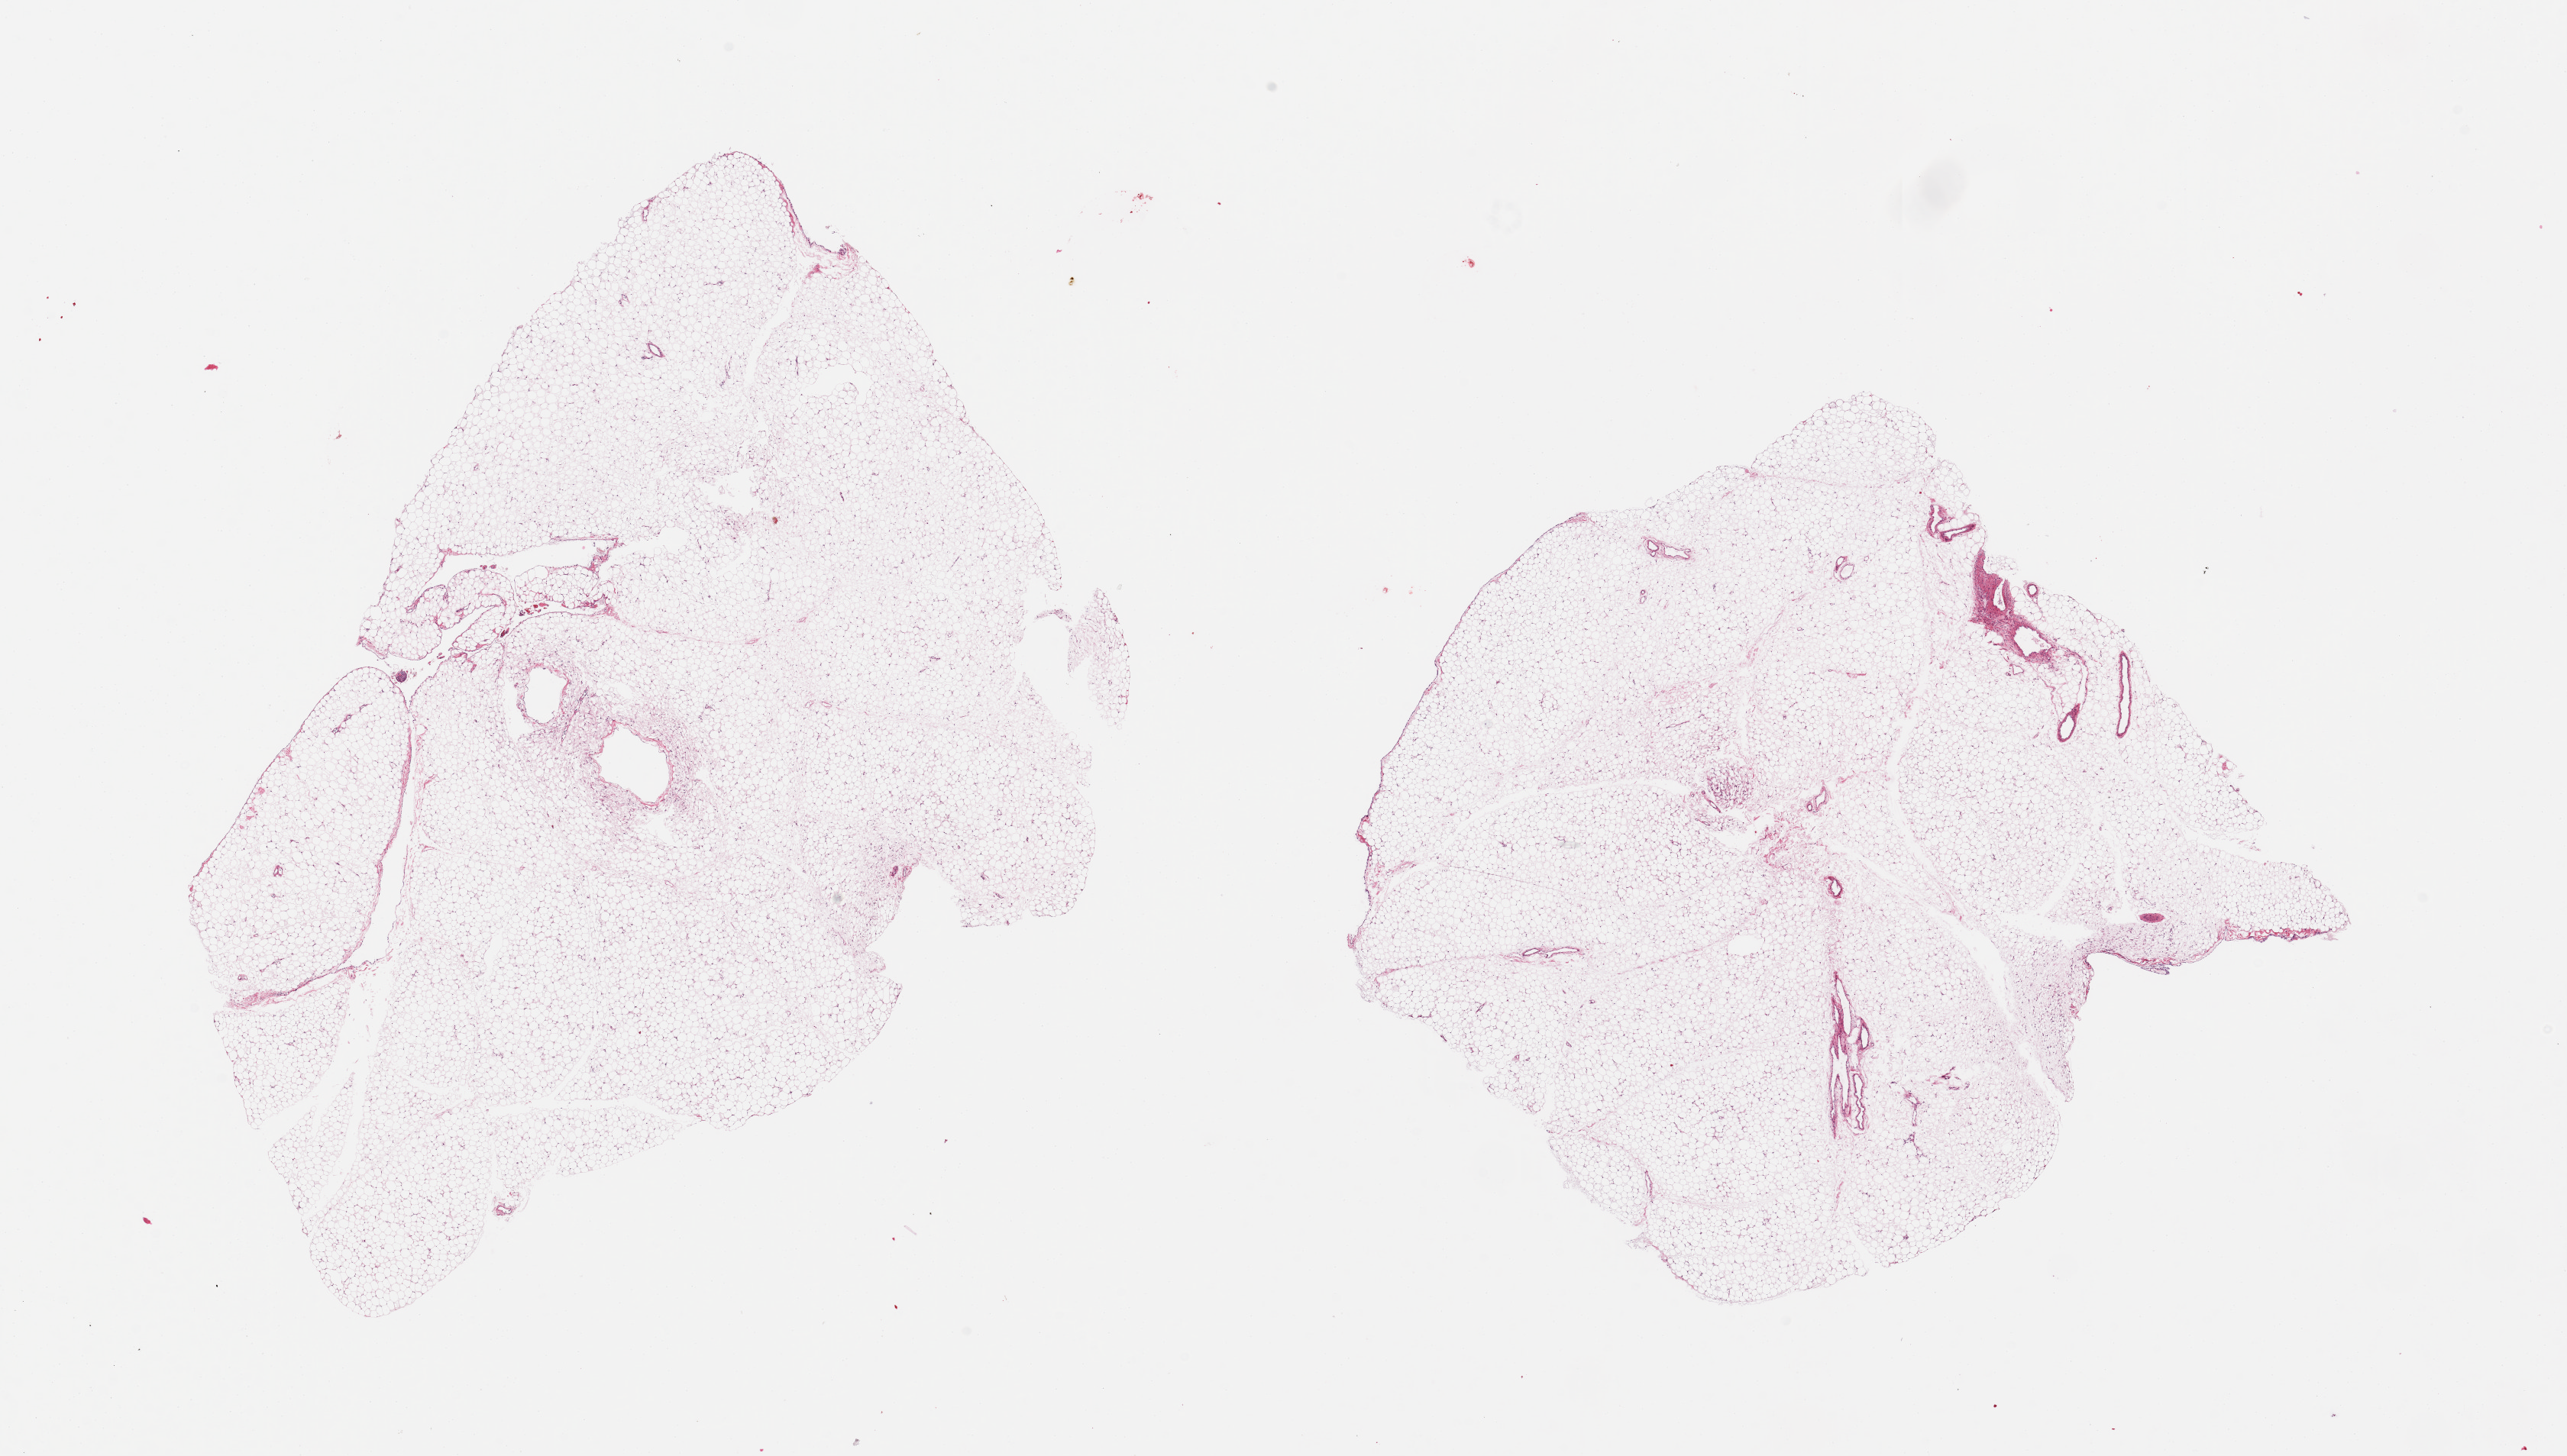
Whole-slide image, H&E stain — a low-resolution overview of the entire scanned area, about 26.6 x 15.1 mm; PAXgene-fixed, paraffin-embedded tissue; target tissue: omentum; tissue donor sample.
Reviewer comment on this tissue sample: 2 pieces; mature adipose tissue with trace of fibrovascular component.